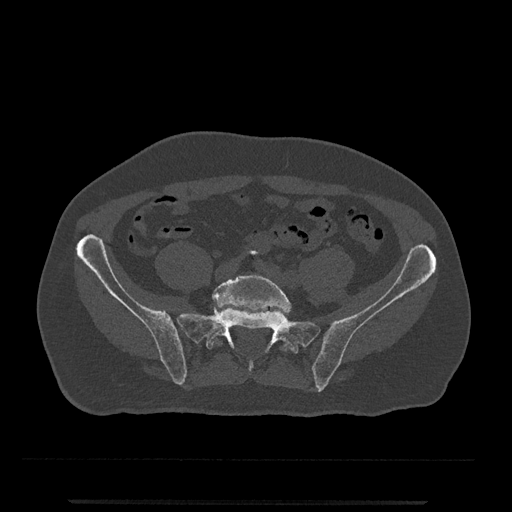
CT including the spine, one axial slice. Slice 36 of 797 in the series (ordered by position). Bone window (W 1800 / L 400 HU). 0.5 mm slice thickness. 512 × 512 image matrix. Male patient, age 63 years. From the clinical record (not read from this slice): primary cancer: prostate.
Outlined on this slice (semi-automatic segmentation, software-assisted and operator-edited):
- L5 vertebra: box from (x=209, y=274) to (x=291, y=352) px